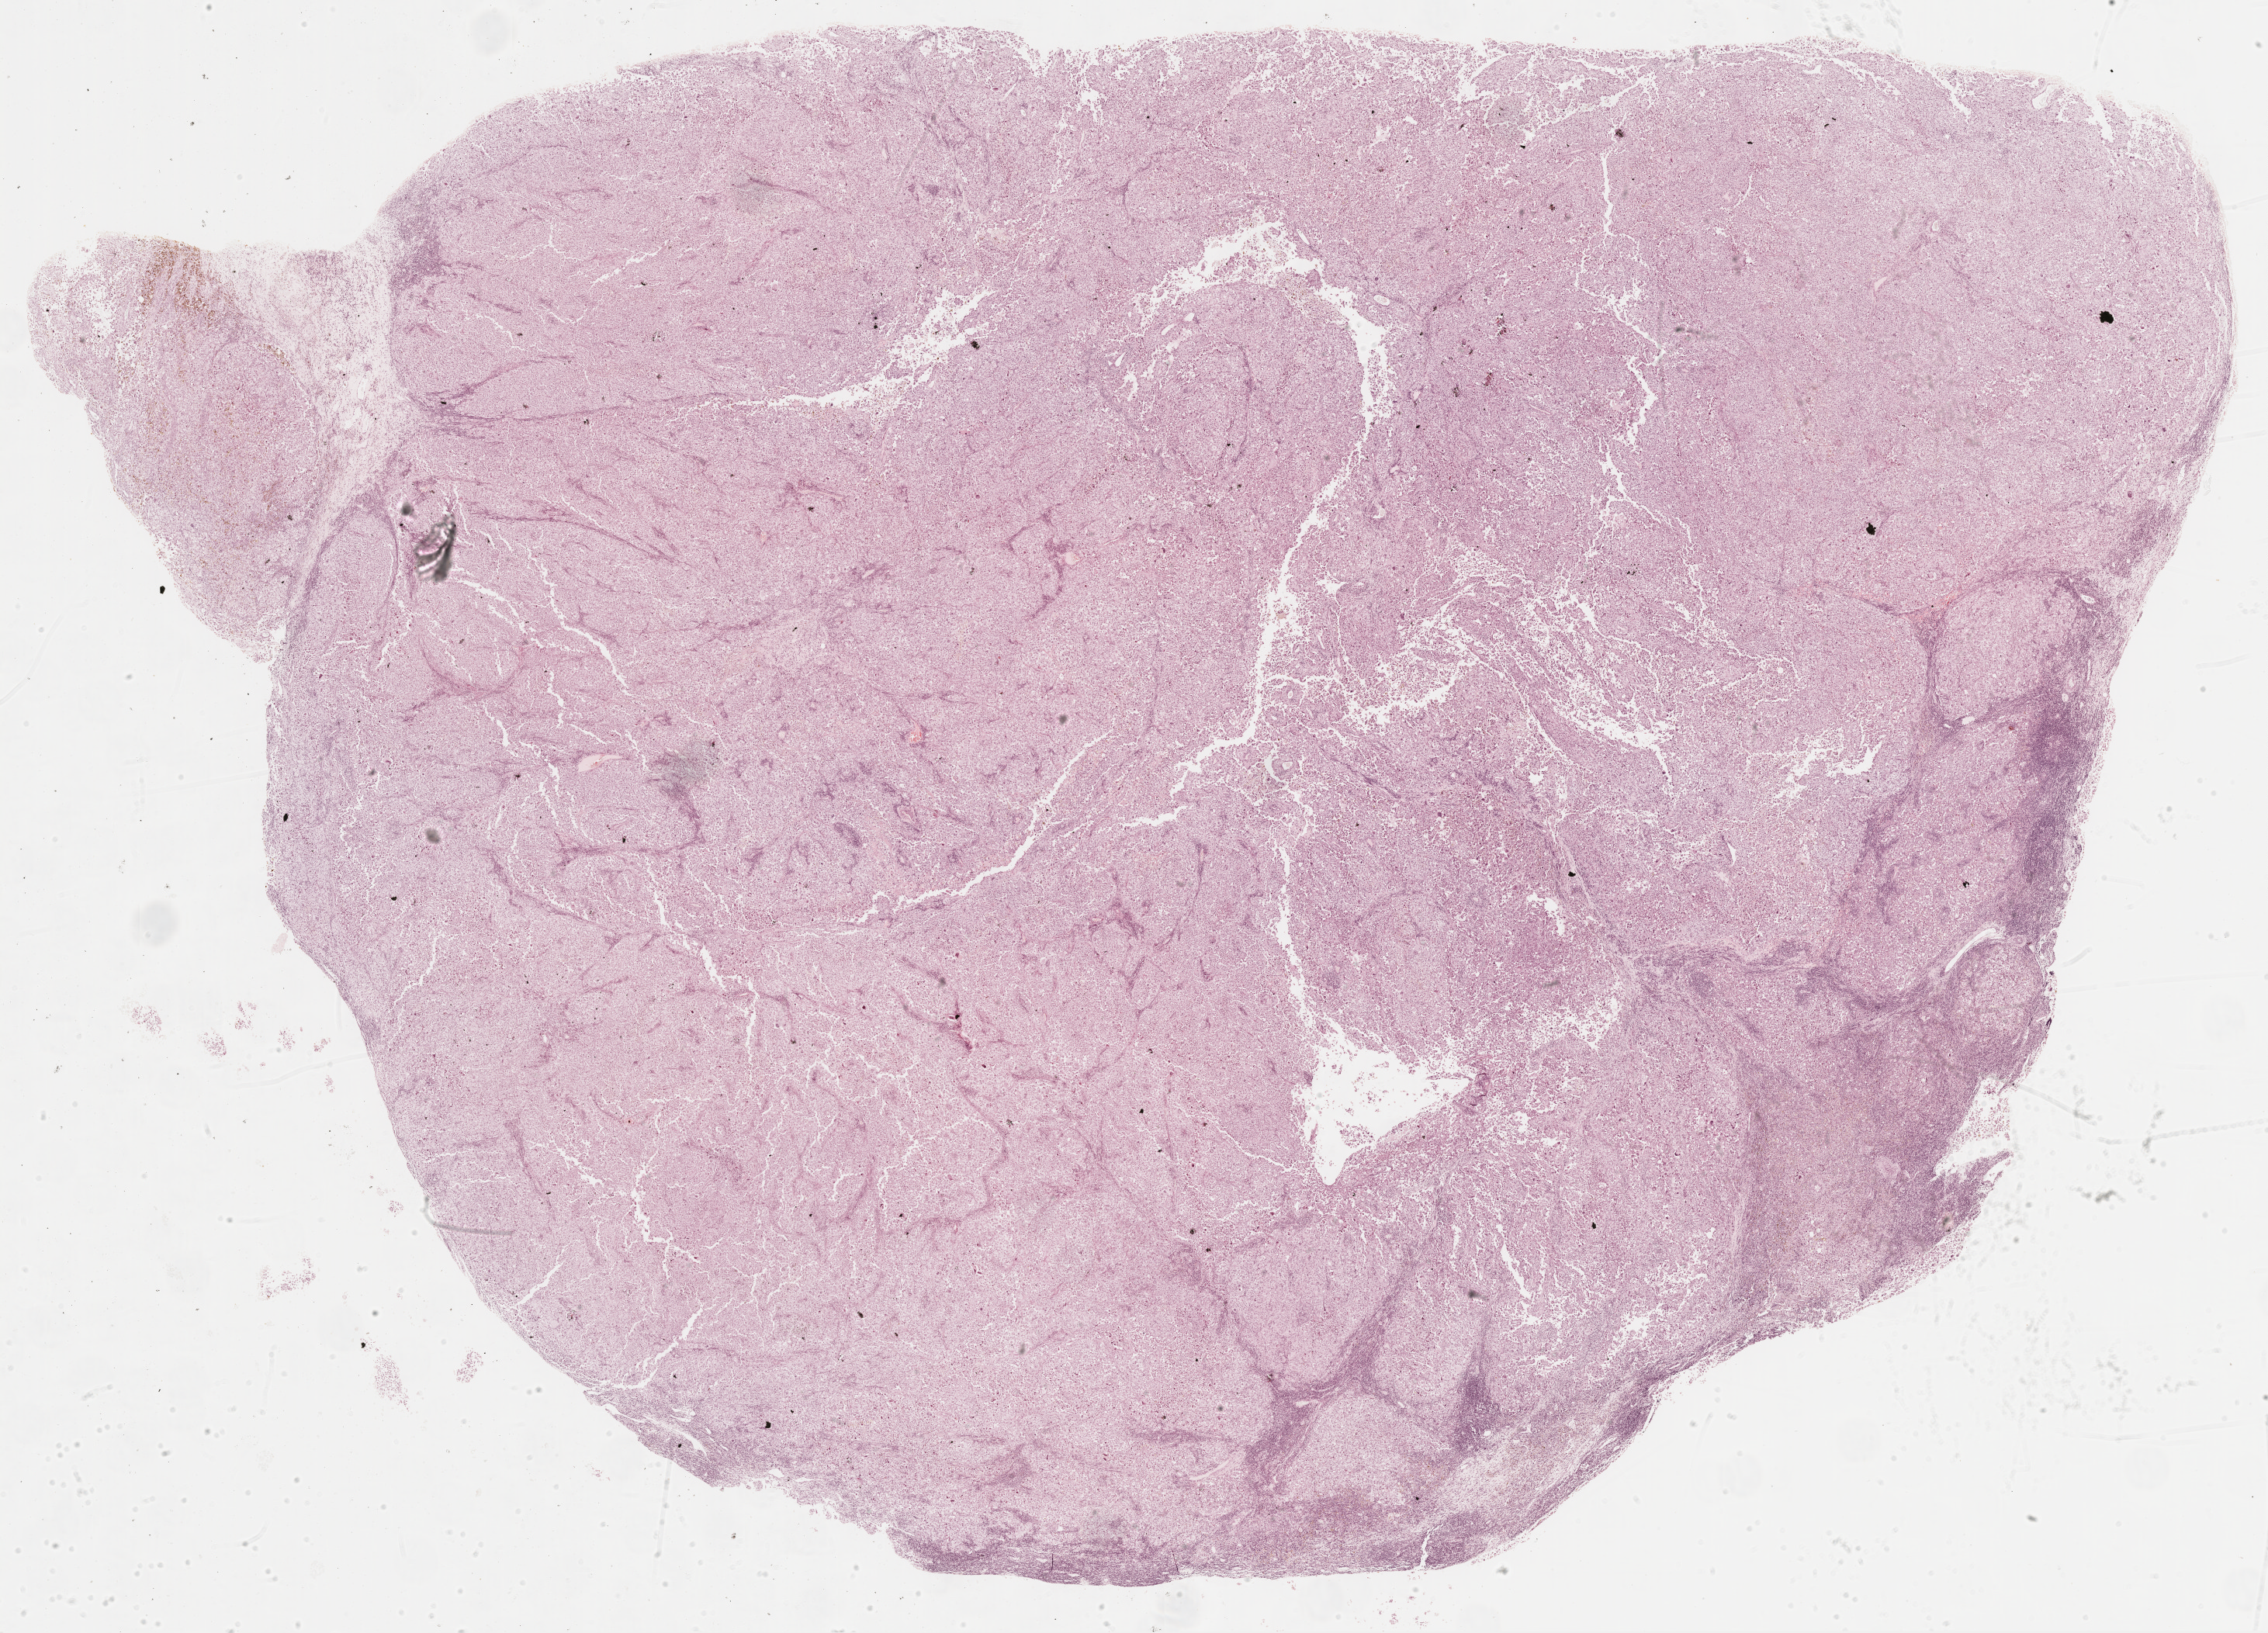
Hematoxylin and eosin (H&E) stained whole-slide image, low-resolution overview of the scanned area, about 23.6 x 17.0 mm (slide scanned at 20x). Formalin-fixed paraffin-embedded (FFPE) diagnostic section. Metastatic tumour sample, sampled site not recorded. Male, age 72 years at initial diagnosis.
This section: metastatic tumour tissue. Patient diagnosis: Malignant melanoma, NOS.